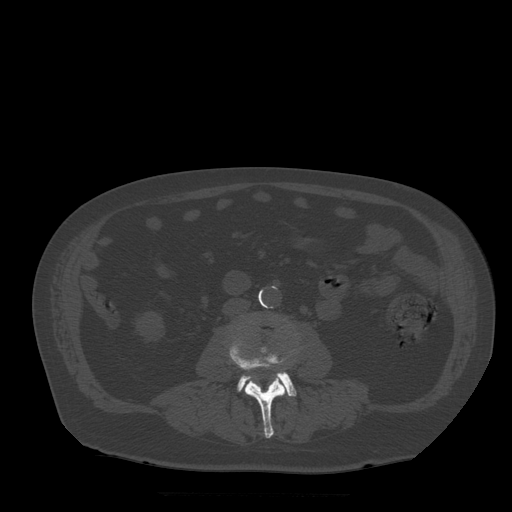
CT including the spine, one axial slice; position 132 of 522 along the scan axis; bone window (W 1800 / L 400 HU); 1.25 mm slice thickness; 512 × 512 image matrix. Patient age 72 years. From the clinical record (not read from this slice): primary cancer: prostate.
Structures marked on this image (semi-automatic segmentation, software-assisted and operator-edited):
- L3 vertebra: bounding box <229,337,286,438> (left, top, right, bottom; pixels)
- L4 vertebra: <238,348,297,396>